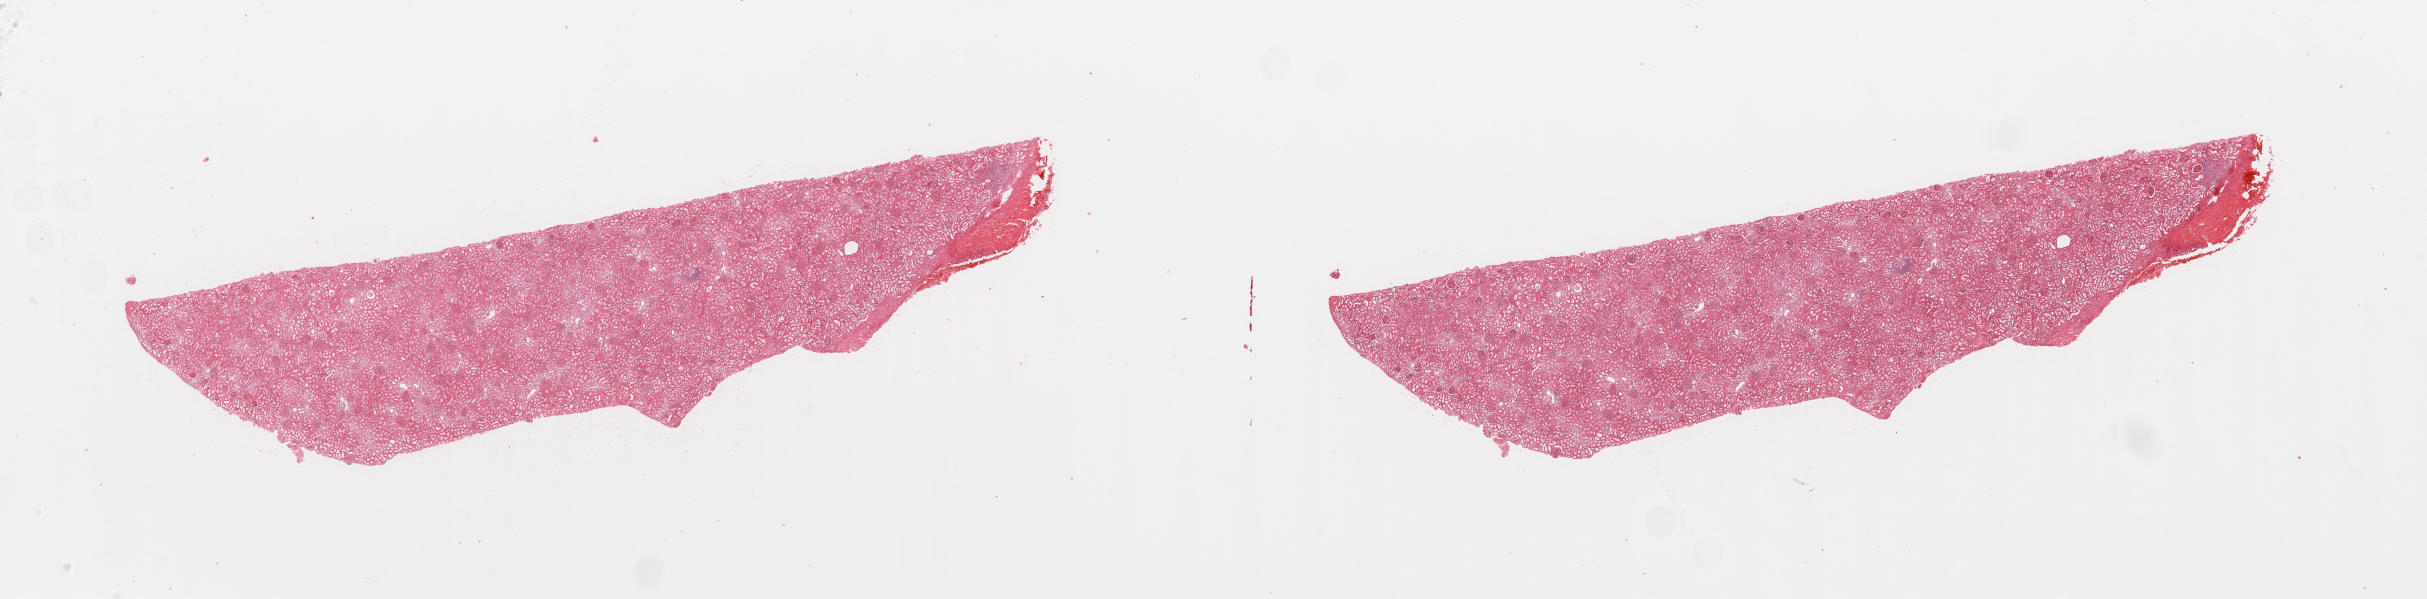
H&E-stained whole-slide image — shown as a low-resolution overview of the whole scanned area (about 38.4 x 9.5 mm). Normal (non-tumour) tissue sample, sampled site: kidney. Male, 47 y/o.
This section: normal (non-tumour) tissue from the same patient. Patient diagnosis: Renal cell carcinoma, NOS.